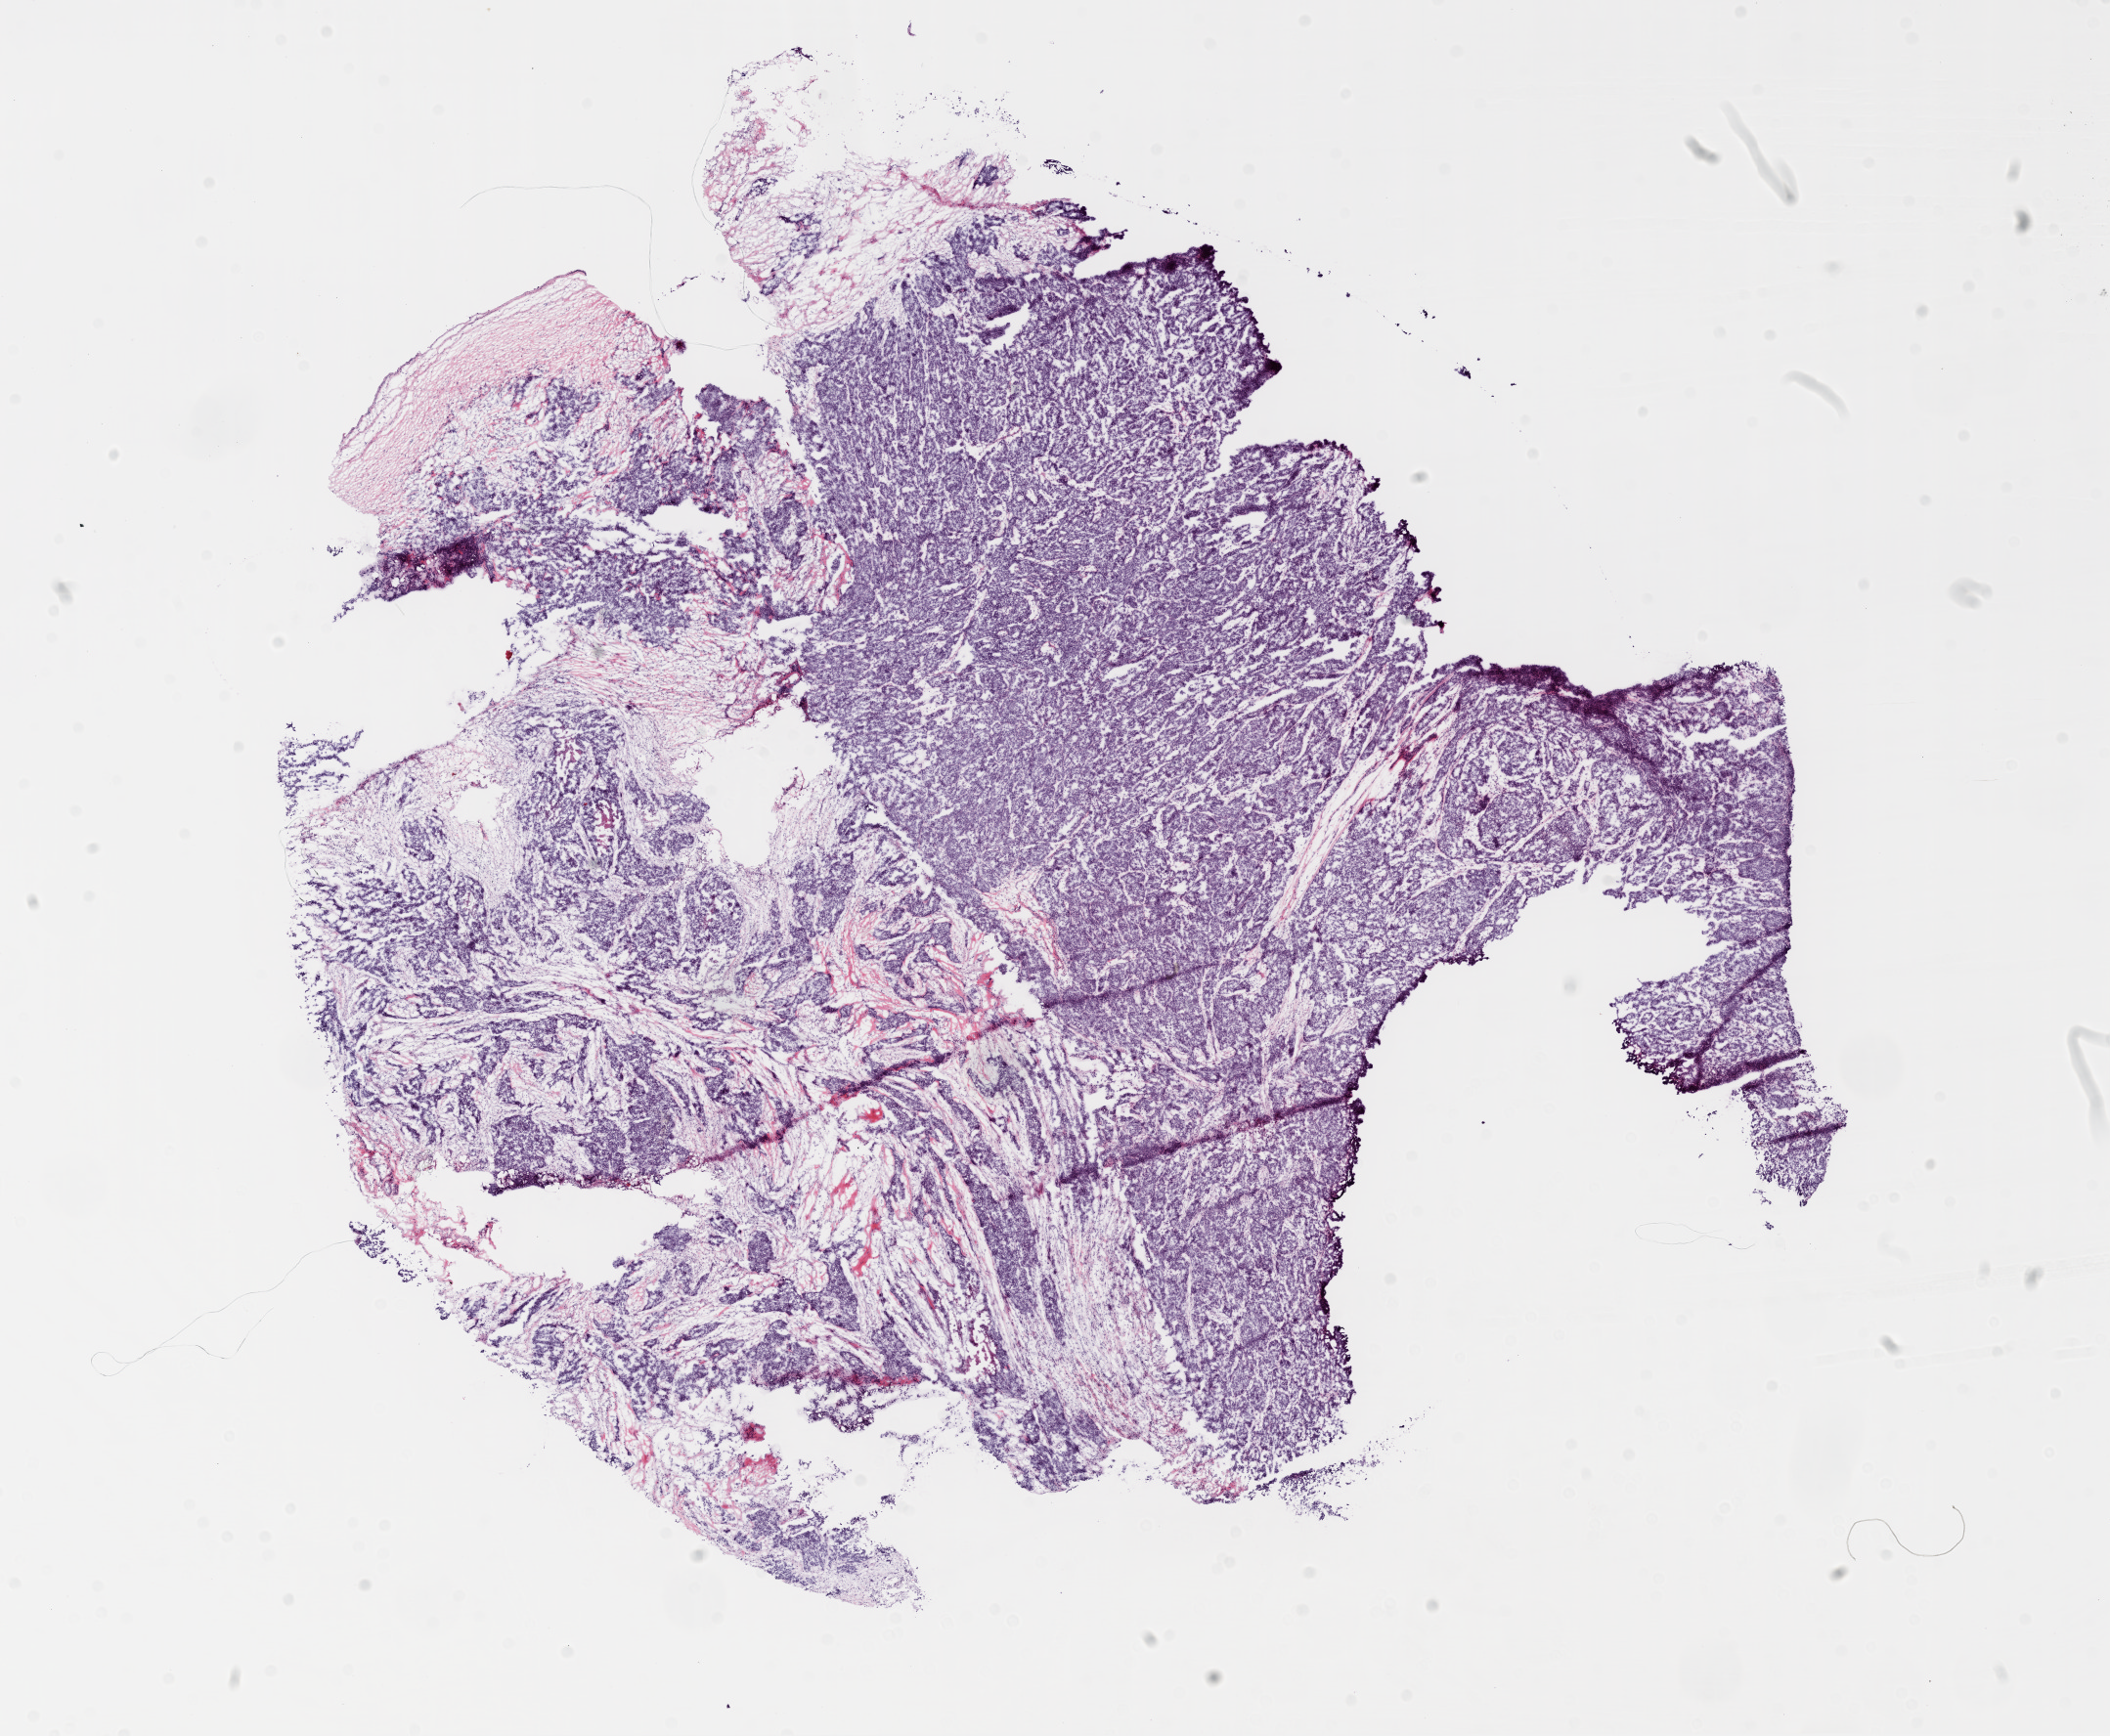
Digitized H&E-stained tissue section (whole slide), whole scanned area (about 17.4 x 14.3 mm, from a 20x scan) shown as a low-resolution overview; frozen section from the top of the tissue portion; sample: primary tumour, ovary. Patient: female, age at initial diagnosis 72 years. Histologic grade: G3 (poorly differentiated). Slide review estimates, as recorded: tumour cells 95%, tumour nuclei 98%, normal cells 0%, stromal cells 5%, necrosis 0%.
Histologic diagnosis: Serous cystadenocarcinoma, NOS. FIGO stage: IV.